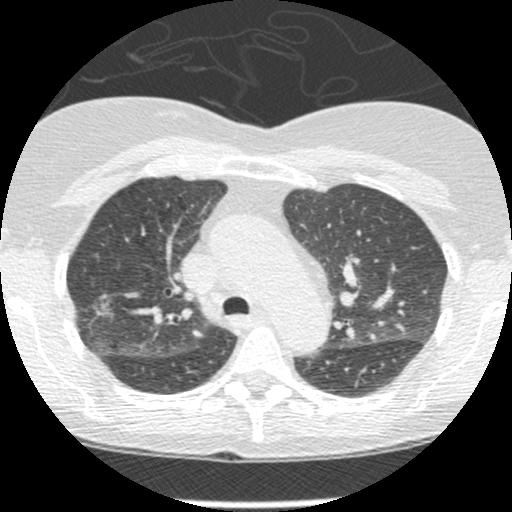
Low-dose screening chest CT, one axial slice. Position 176 of 238 along the scan axis. Reconstruction kernel STANDARD. Lung window (W 1500 / L -600 HU). 1.25 mm slice thickness. 512 × 512 image matrix.
Outlined on this slice (manually delineated by an expert):
- lesion 1 (tumor, upper lobe of right lung): bounding box (x1, y1, x2, y2) in pixels: (97, 304, 111, 316)